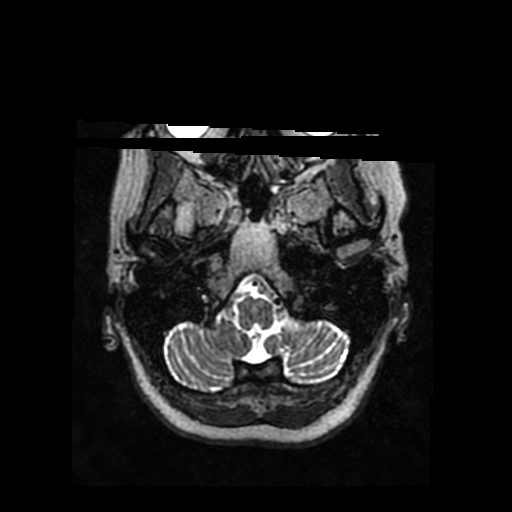
Brain MRI from a brain-tumour surgery series, one axial slice. 512 × 512 image matrix, field of view 240 × 240 mm. From the clinical record (not read from this slice): histopathology: Glioblastoma; WHO grade: 4; IDH mutation: no.
Structures marked on this image (expert manual segmentation):
- tumour: bounding box [x1, y1, x2, y2] px = [201, 204, 209, 219]